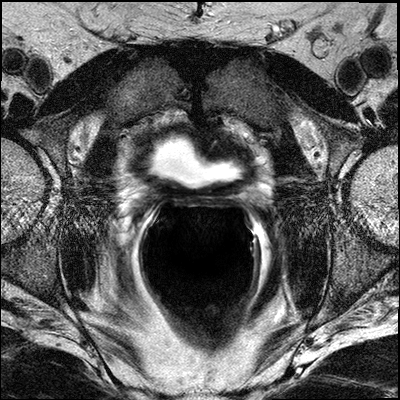
MRI of the prostatic bed after radical prostatectomy; 3 images, each a single mid-volume slice chosen by position (not for content). Treatment context recorded for this patient: Post-op.
Image 1: T2-weighted axial slice, series "T2W_TSE_AX", slice 19 of 36.
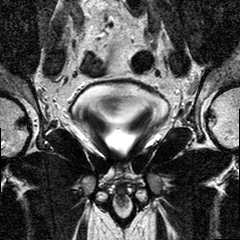
Image 2: coronal T2-weighted image, series "T2W_TSE_COR", slice 14 of 26, 3 mm slice thickness.
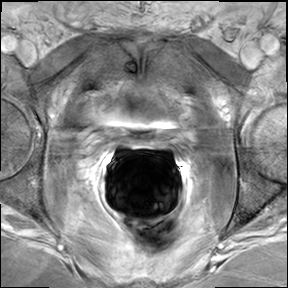
Image 3: DCE (dynamic gadolinium-enhanced) axial slice, series "AX BLISS_GAD_8", slice 18 of 34, dynamic phase 5 of 8.
Radiologist's MRI report for this examination:
FINDINGS: Regular findings seen within the surgical bed. Multiple surgical clips within the prostatic bed and around the anastomosis. Regular appearance of the anastomosis. No definite masses seen within the prostatic bed. No foci of suspicious enhancement in and around the prostatic bed. Unremarkable urinary bladder. No remnant seminal vesicles present. No suspiciously enlarged obturator and iliac lymph nodes. No suspicious the enlarged lymph nodes seen along the iliac vessel, or obturator stations. The left femur head shows a rounded T1-W hypo intense circumscribed lesion; a possible smaller lesion of similar signal is seen in the right femur head. Several small areas of signal changes on T2-W and T1 are seen in the pelvic ring. None of the lesions is completely characterized (either in the field of view only on one sequence, or not on contrast enhanced images) Further imaging needed. IMPRESSION:No suspicious mass in the surgical bed; no enlarged obturator or iliac lymph nodes. Normal appearance of the prostatic bed and anastomosis.Suspicious incompletely characterized bone lesions in the pelvic ring (especially left femur head) for which further evaluation is needed with PET/ diagnostic CT or SPECT.